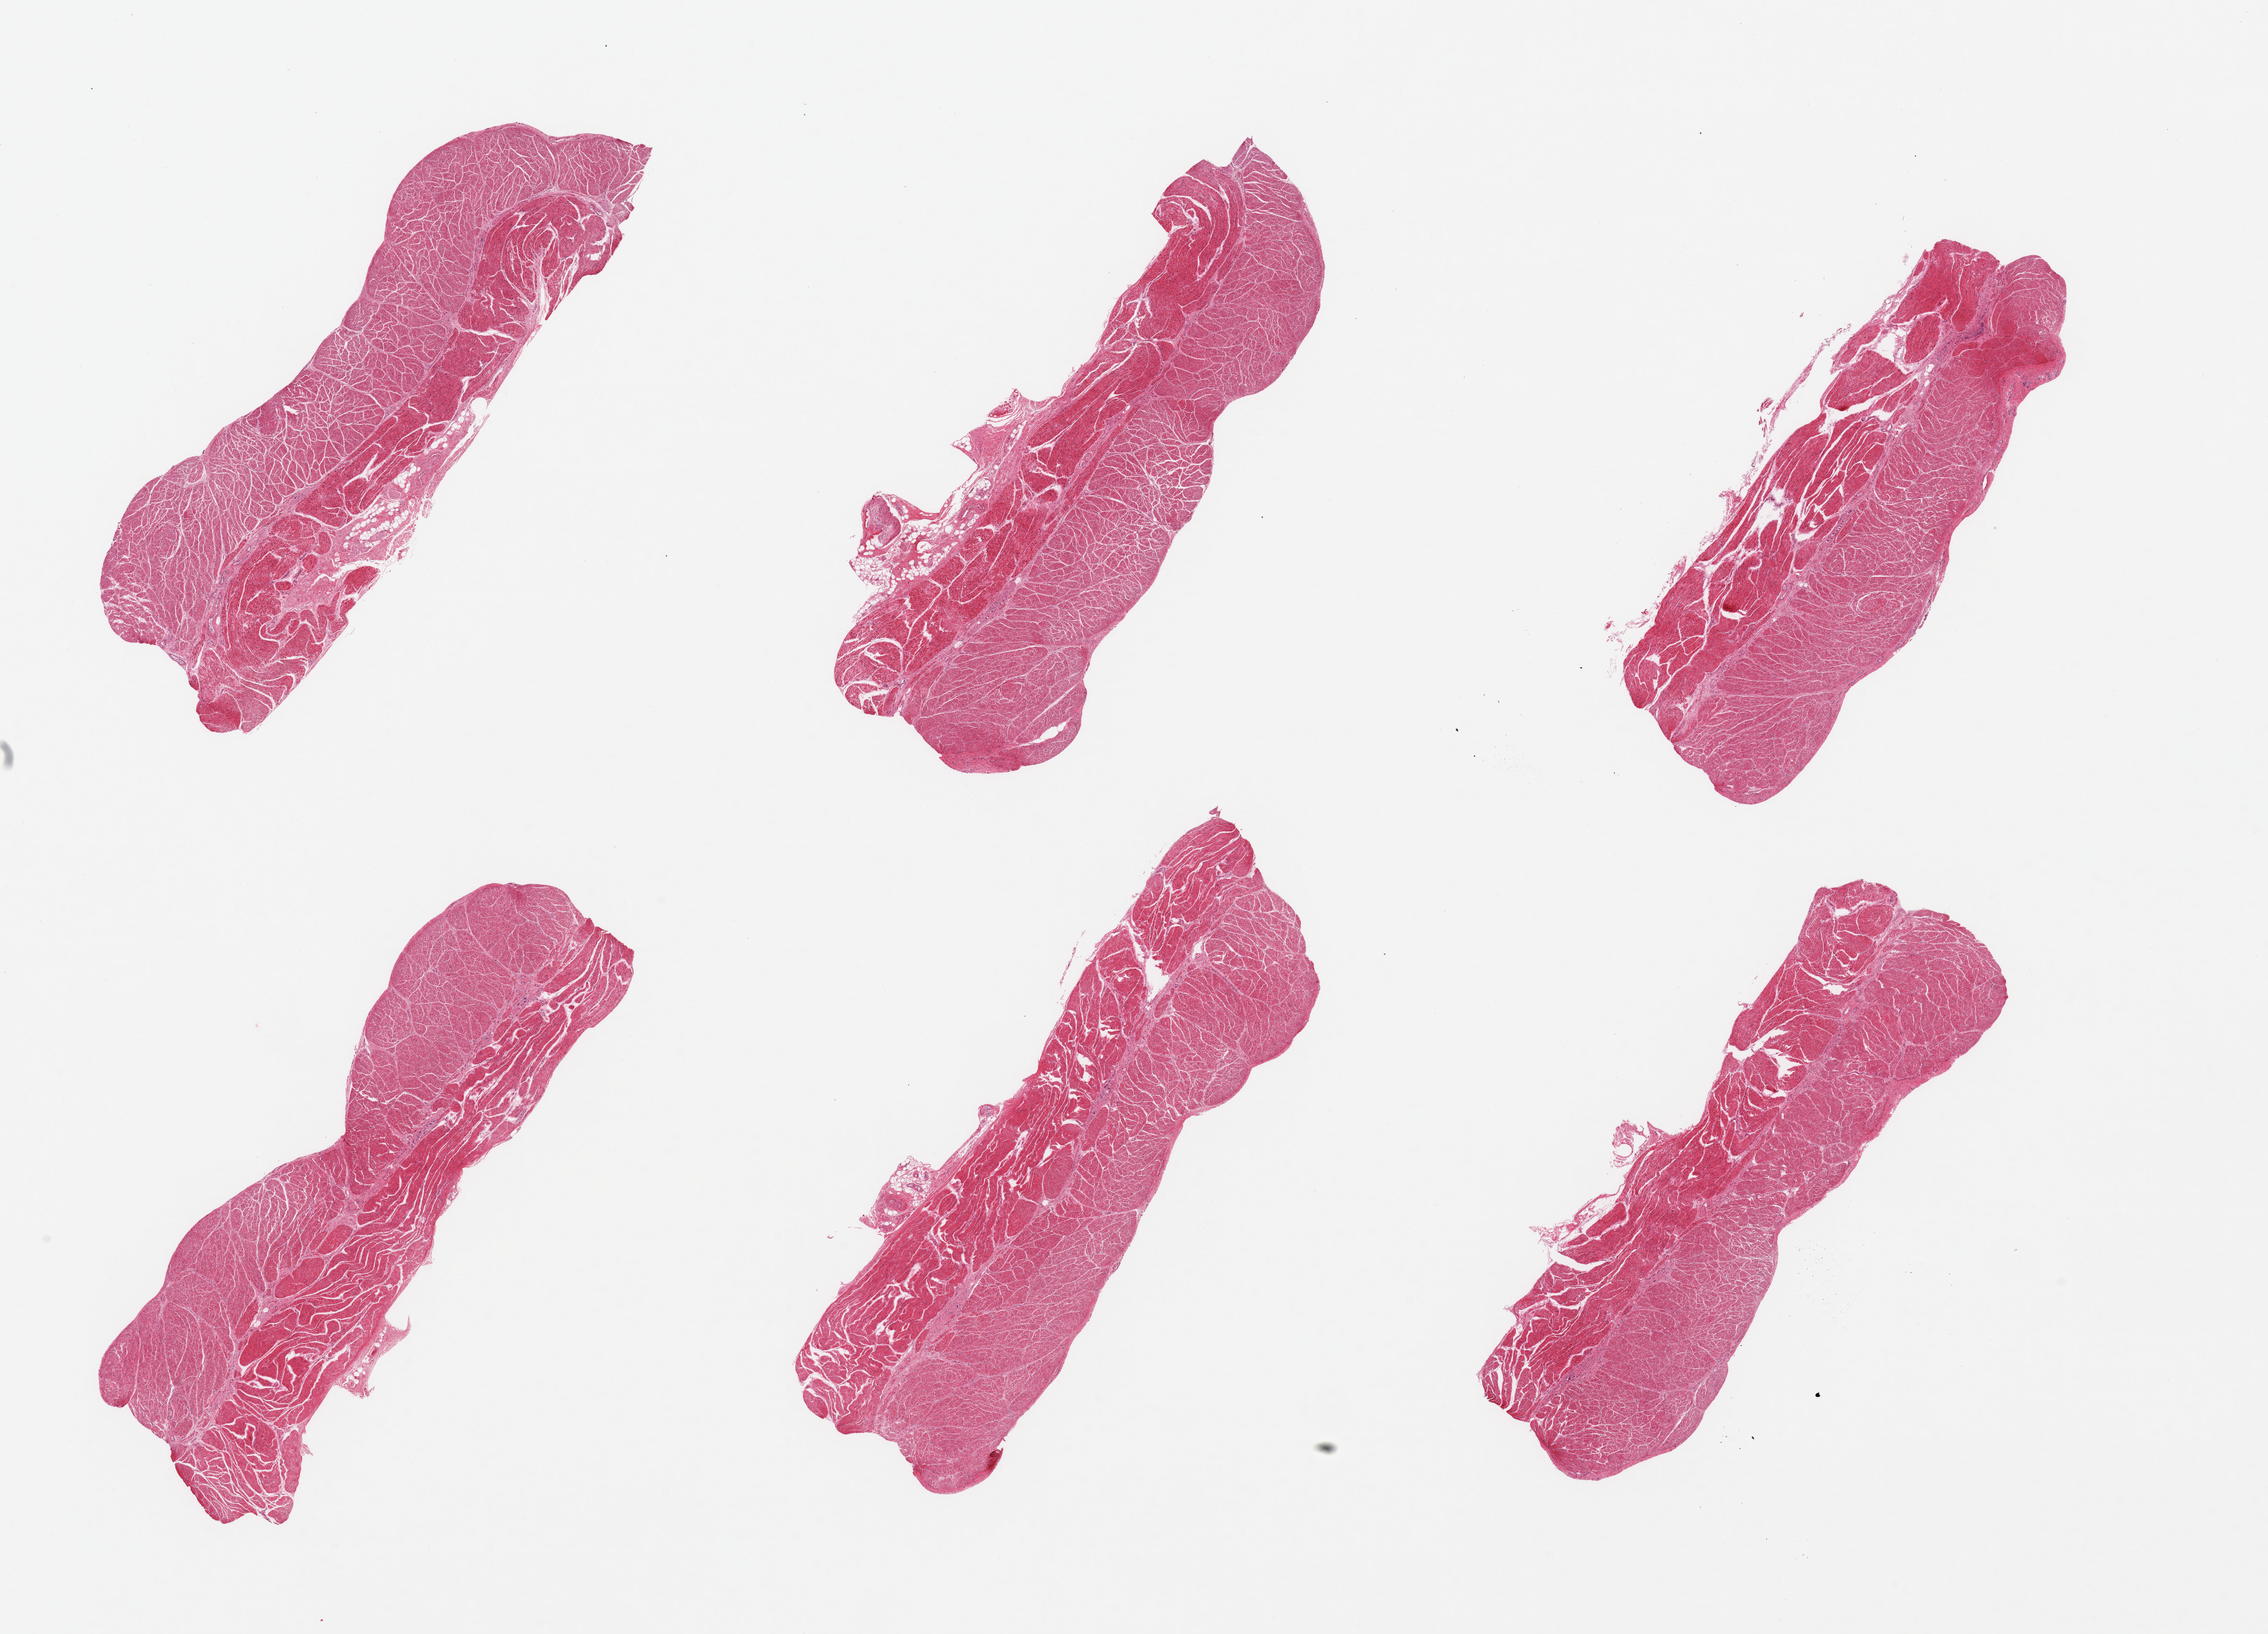
Hematoxylin and eosin (H&E) whole-slide image — whole scanned area (about 25.6 x 18.4 mm, acquisition: 20x scan) shown as a low-resolution overview. PAXgene-fixed, paraffin-embedded tissue. Sampled site (target tissue): gastroesophageal junction. Tissue donor sample. Female donor.
Reviewer comment on this tissue sample: 6 pieces, confirmed target muscularis.